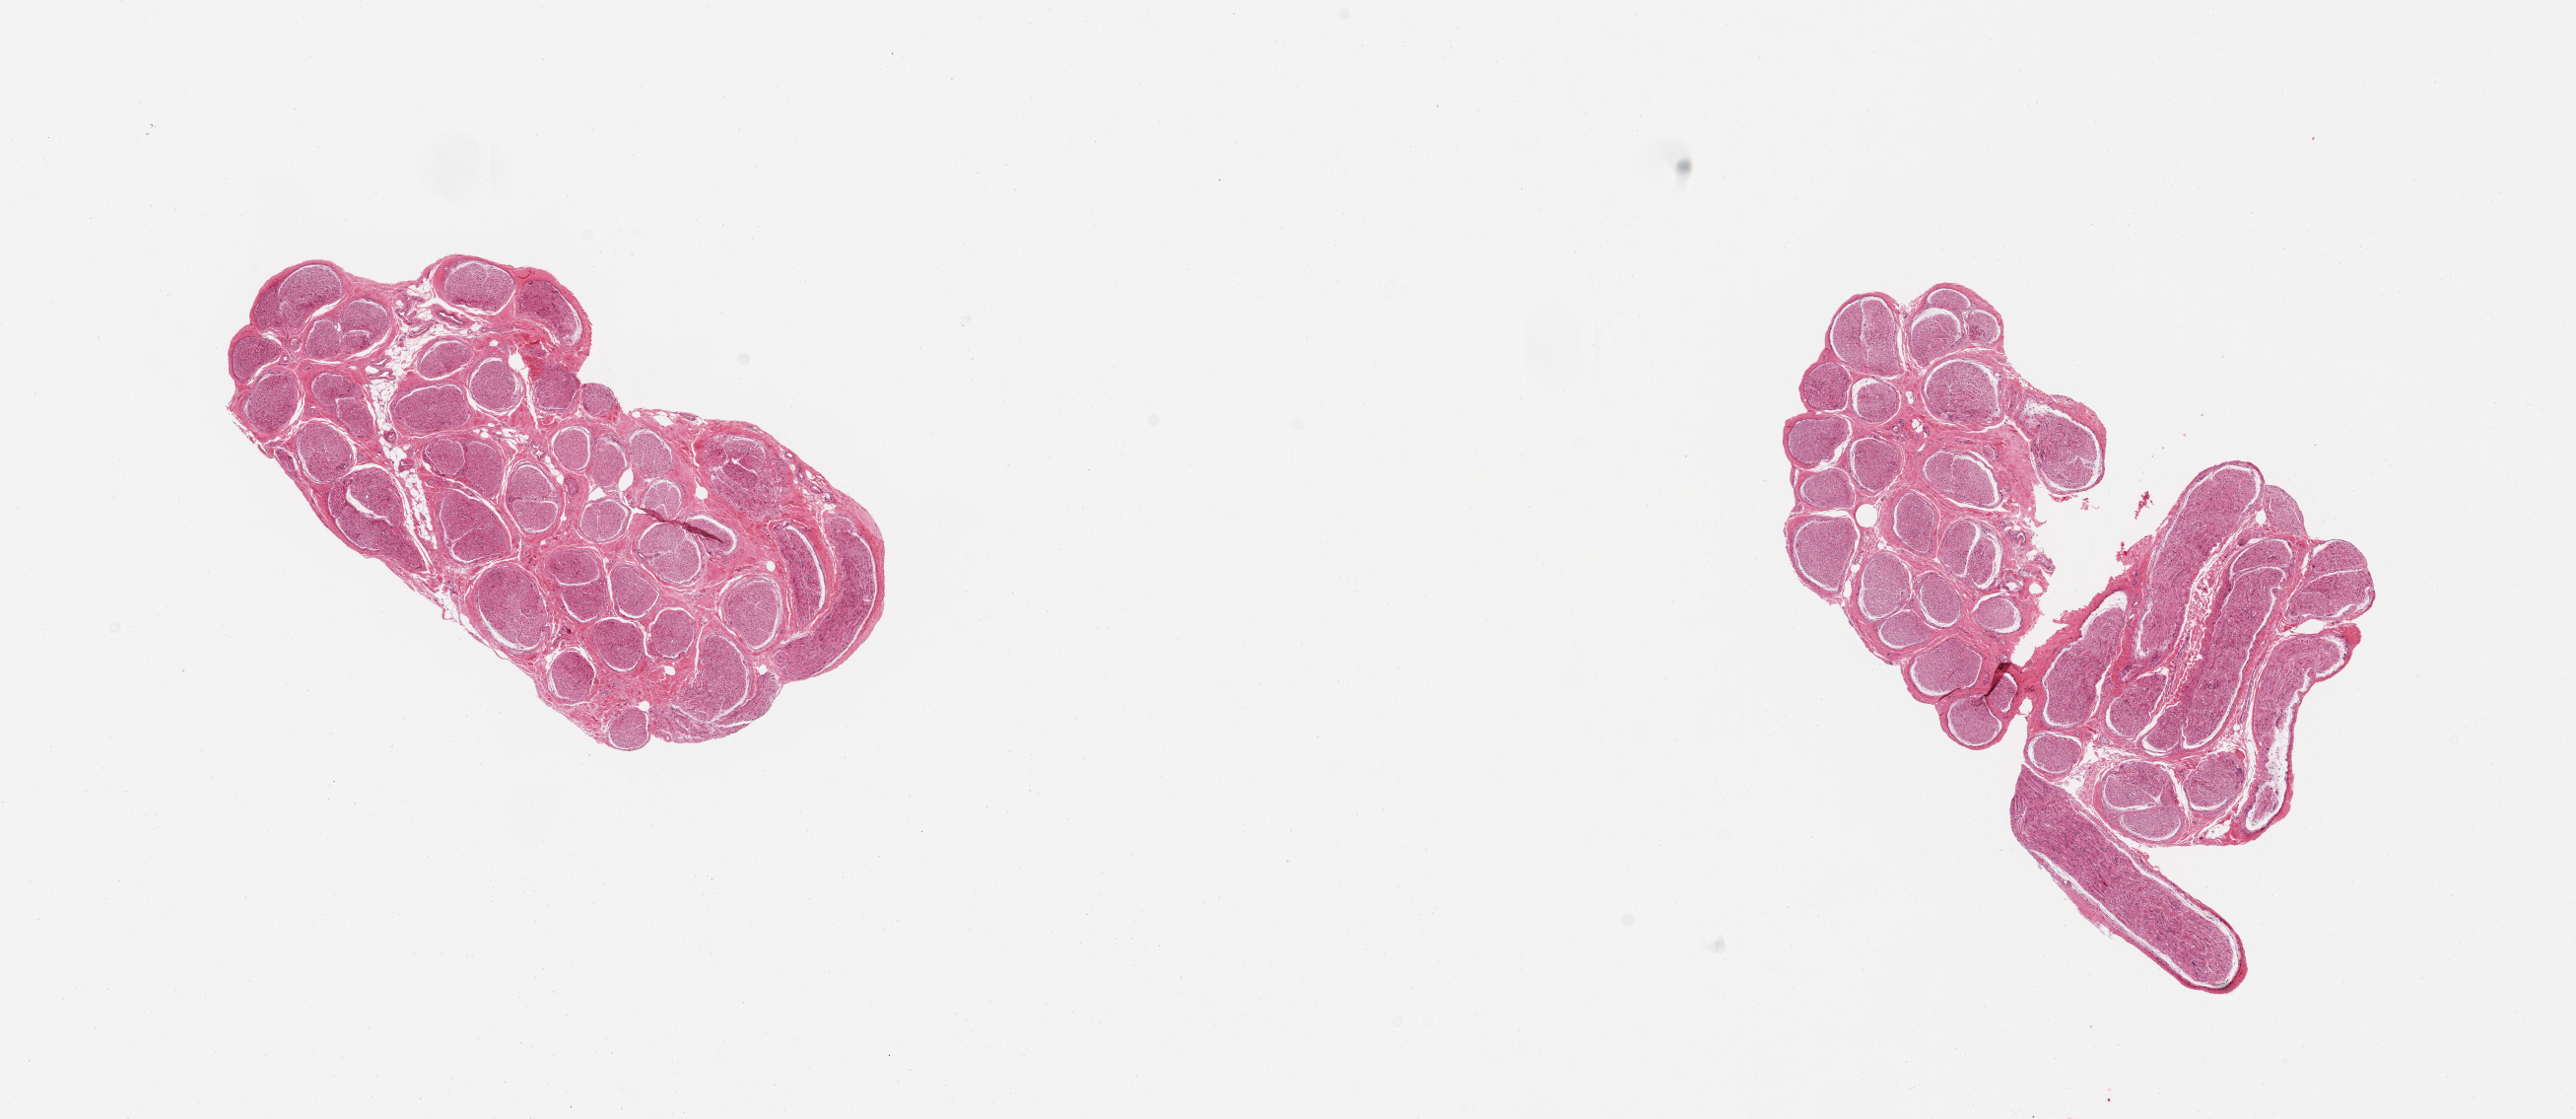
H&E whole-slide image, shown as a low-resolution overview of the whole scanned area (about 20.7 x 9.0 mm); PAXgene-fixed, paraffin-embedded tissue; sampled site (target tissue): tibial nerve; donor tissue sample.
Pathologist's review note for this sample: 2 pieces; well trimmed; <5% fat.